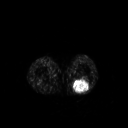
FDG PET of an extremity soft-tissue mass (from a PET/CT study), one axial slice. Slice 188 of 267 in the series (ordered by position). 3.27 mm slice thickness. 128 × 128 image matrix. Male patient, age 54 years. From the clinical record (not read from this slice): histological type: synovial sarcoma; site of the primary tumour: left poplietal fossa.
Structures marked on this image (expert contour drawn on MRI and transferred to this co-registered scan by the dataset authors):
- gross tumour volume (mass): bounding box [x1, y1, x2, y2] px = [72, 78, 90, 93]